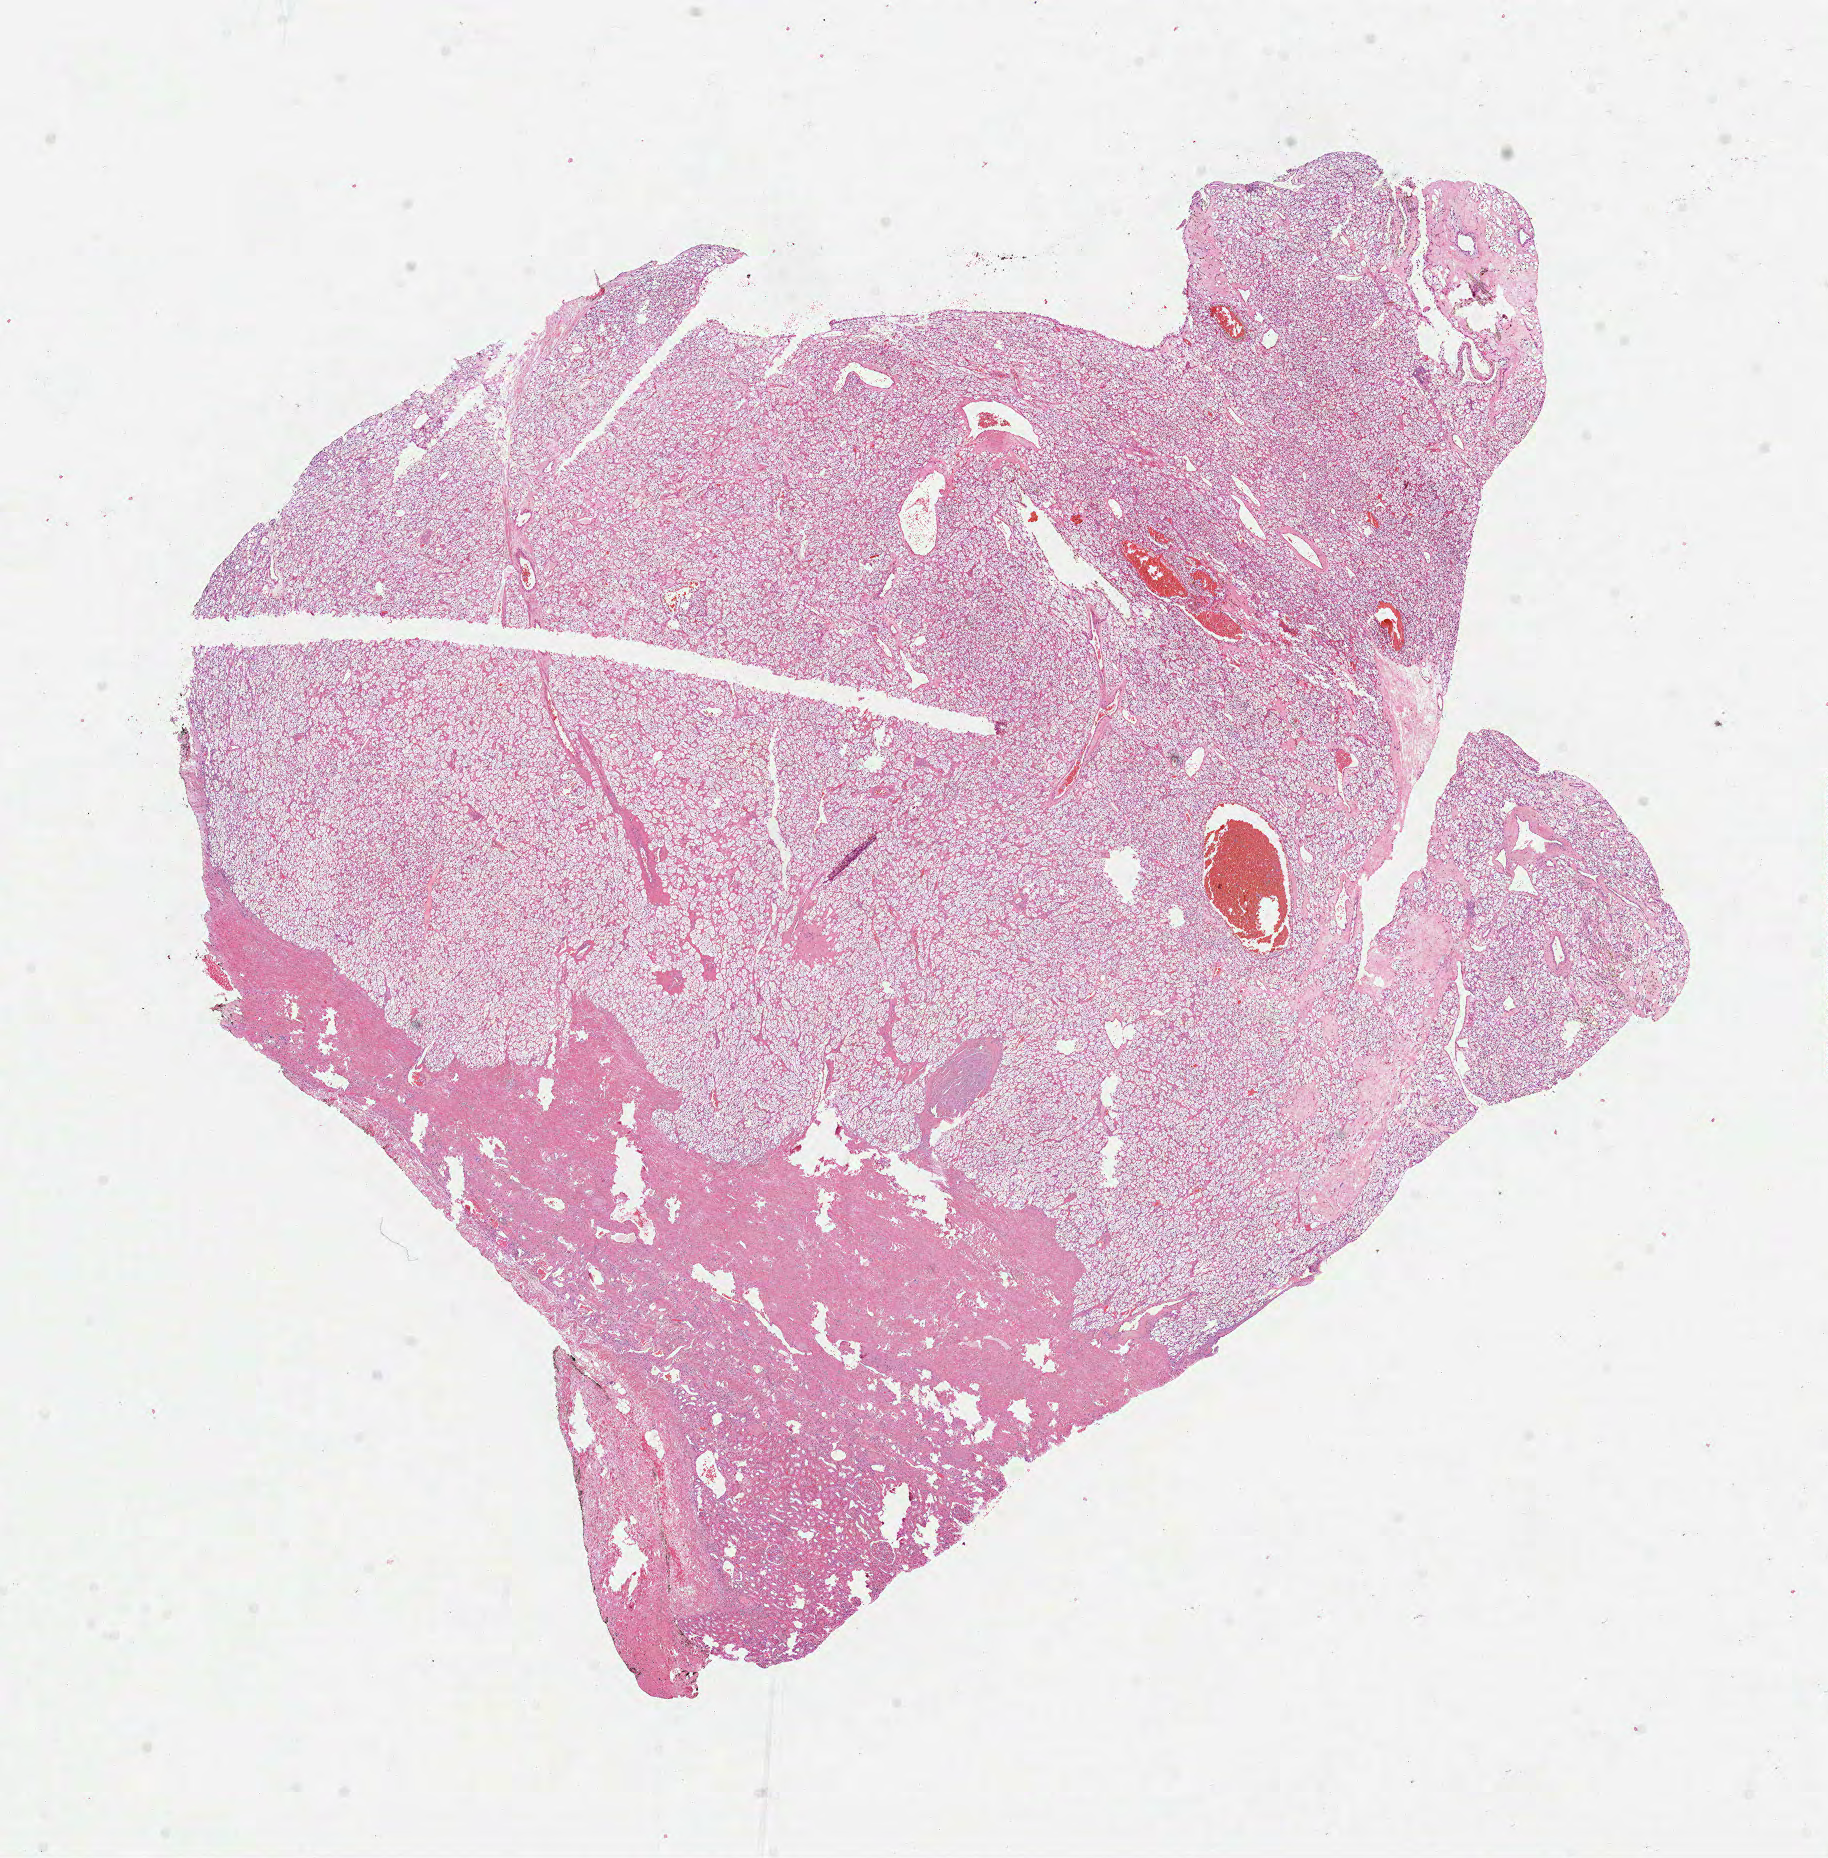
Hematoxylin and eosin (H&E) stained whole-slide image — low-resolution overview of the scanned area, about 14.7 x 15.0 mm (slide scanned at 40x). Formalin-fixed paraffin-embedded (FFPE) diagnostic section. Primary tumour sample from the kidney. Patient: male, age at initial diagnosis 54 years. Histologic grade: G2 (moderately differentiated).
• AJCC pathologic stage: I
• laterality: left
• histologic diagnosis: Clear cell adenocarcinoma, NOS
• TNM: T1 N0 M0